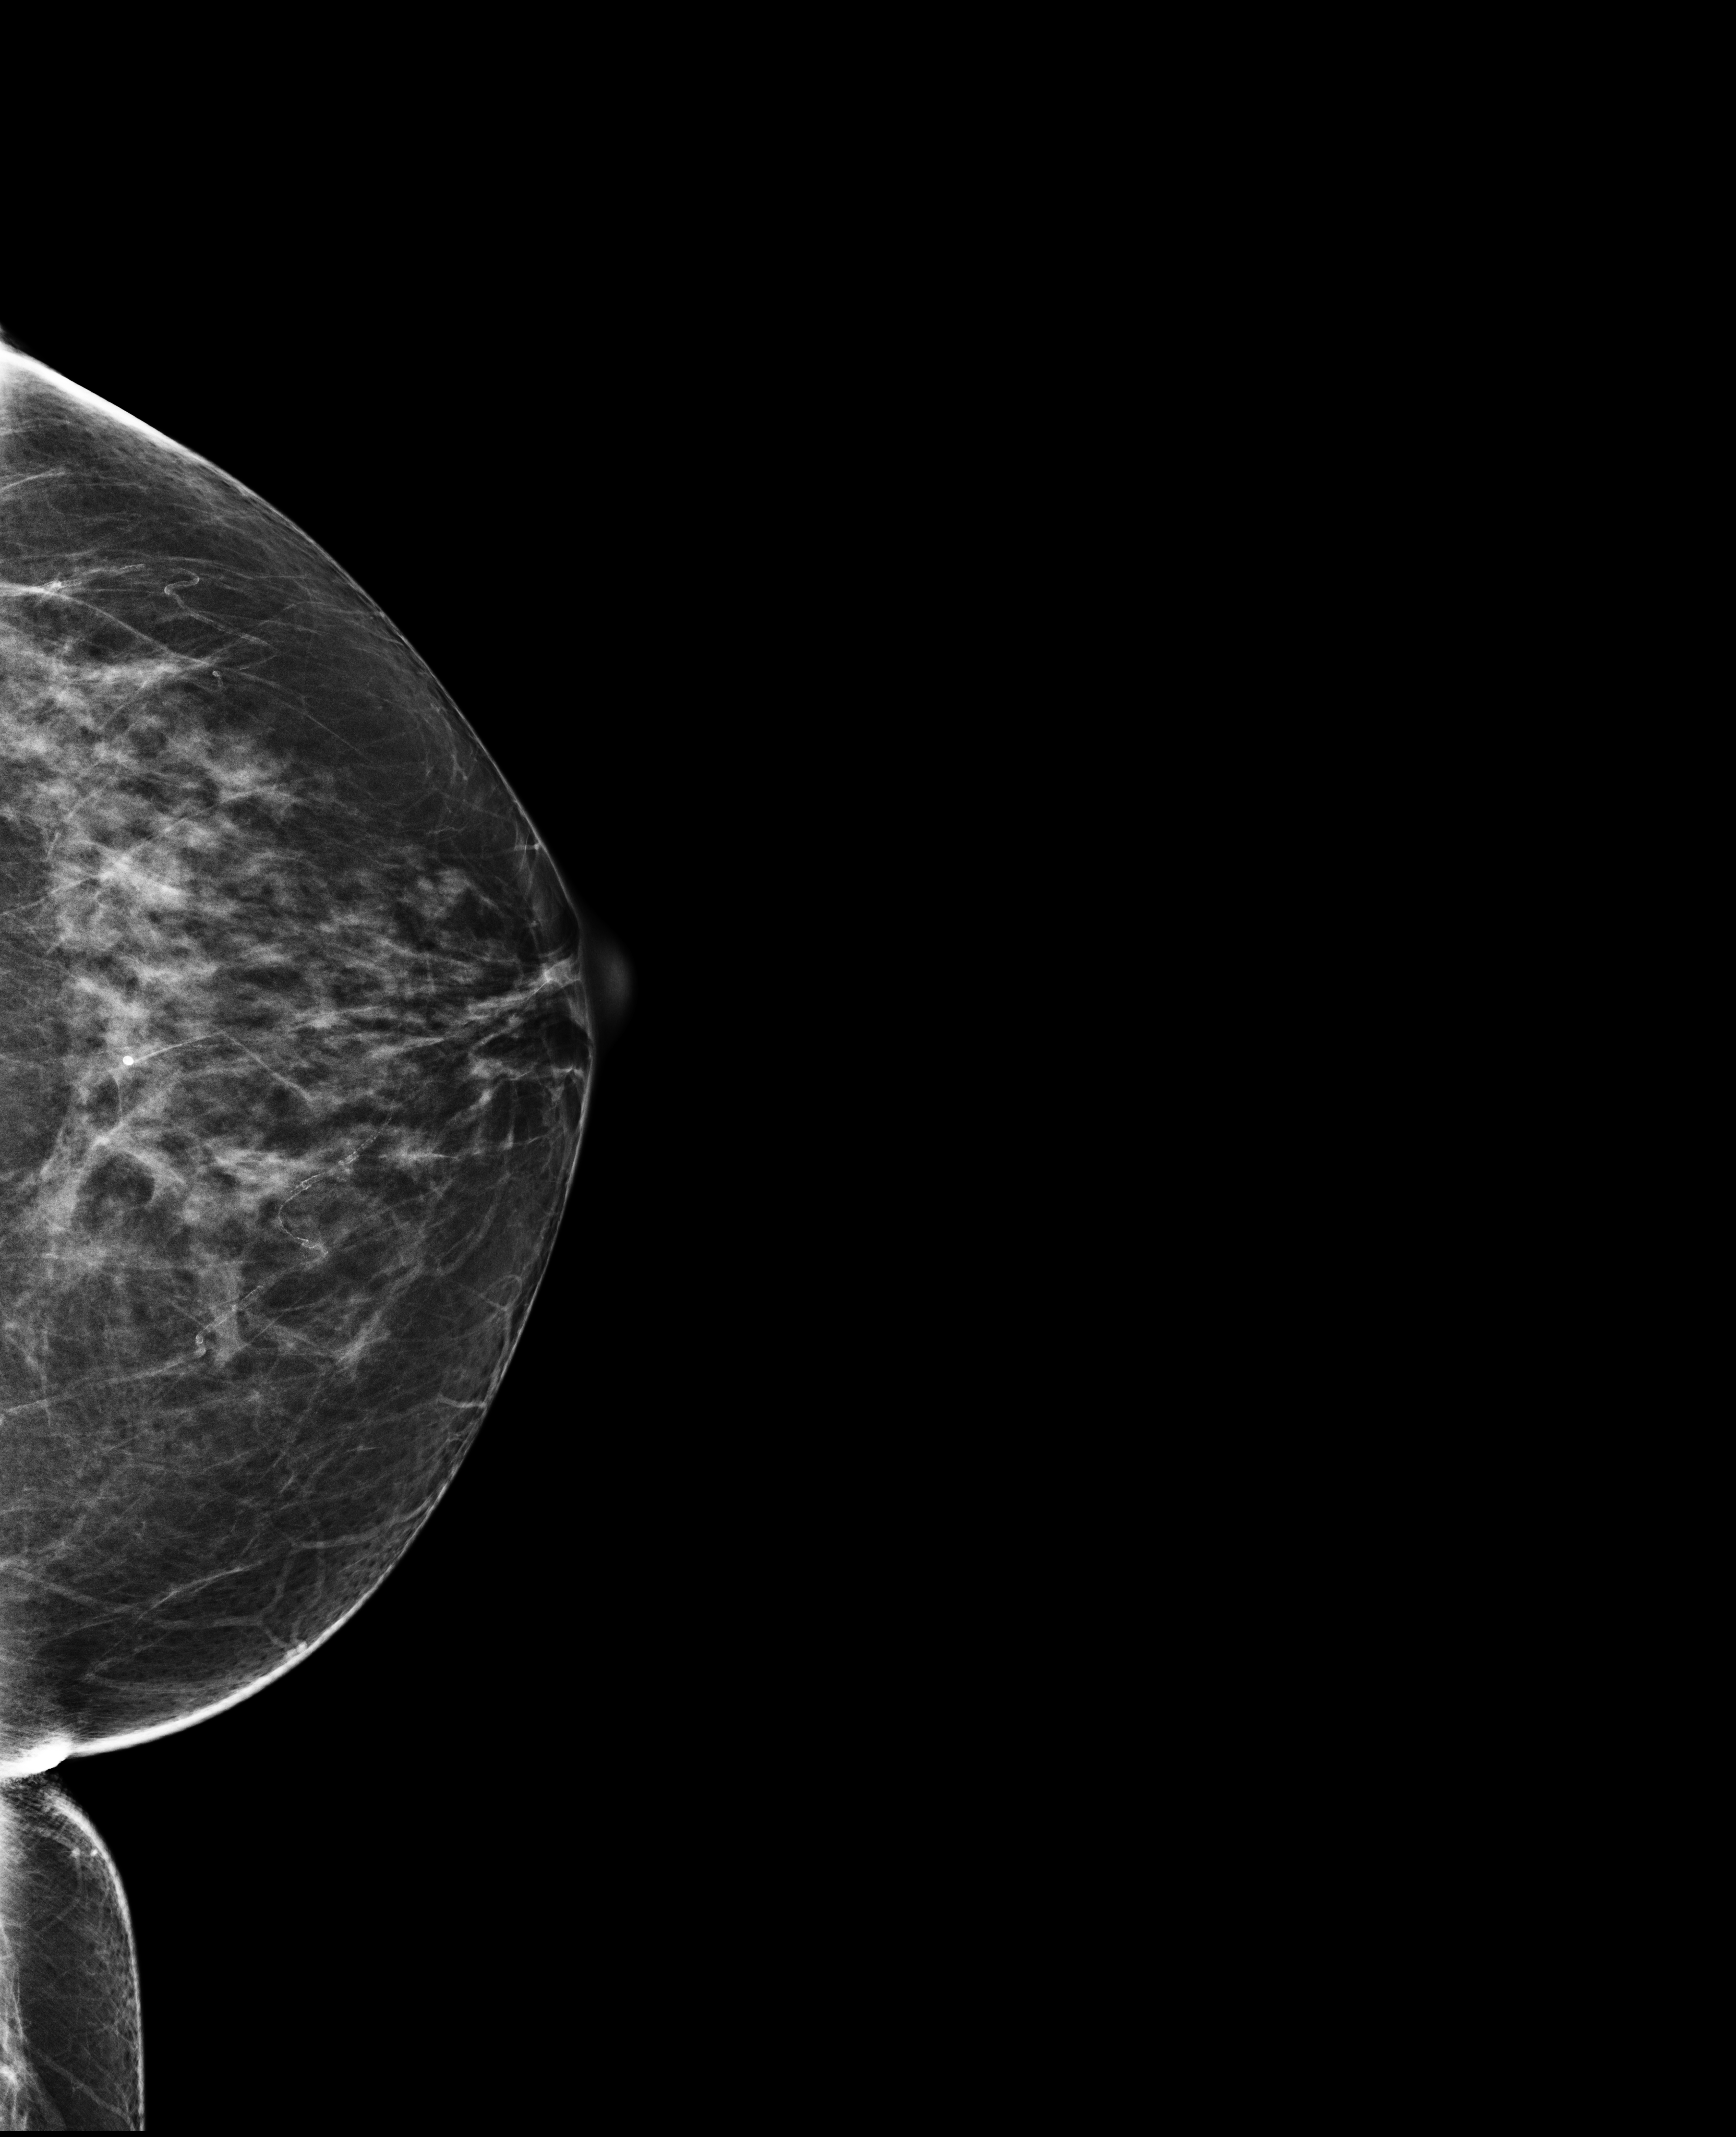
Screening examination, system: Selenia Dimensions. Patient aged 68 years (female).
Image type: full-field digital mammogram. Breast: left. Projection: cranio-caudal projection.